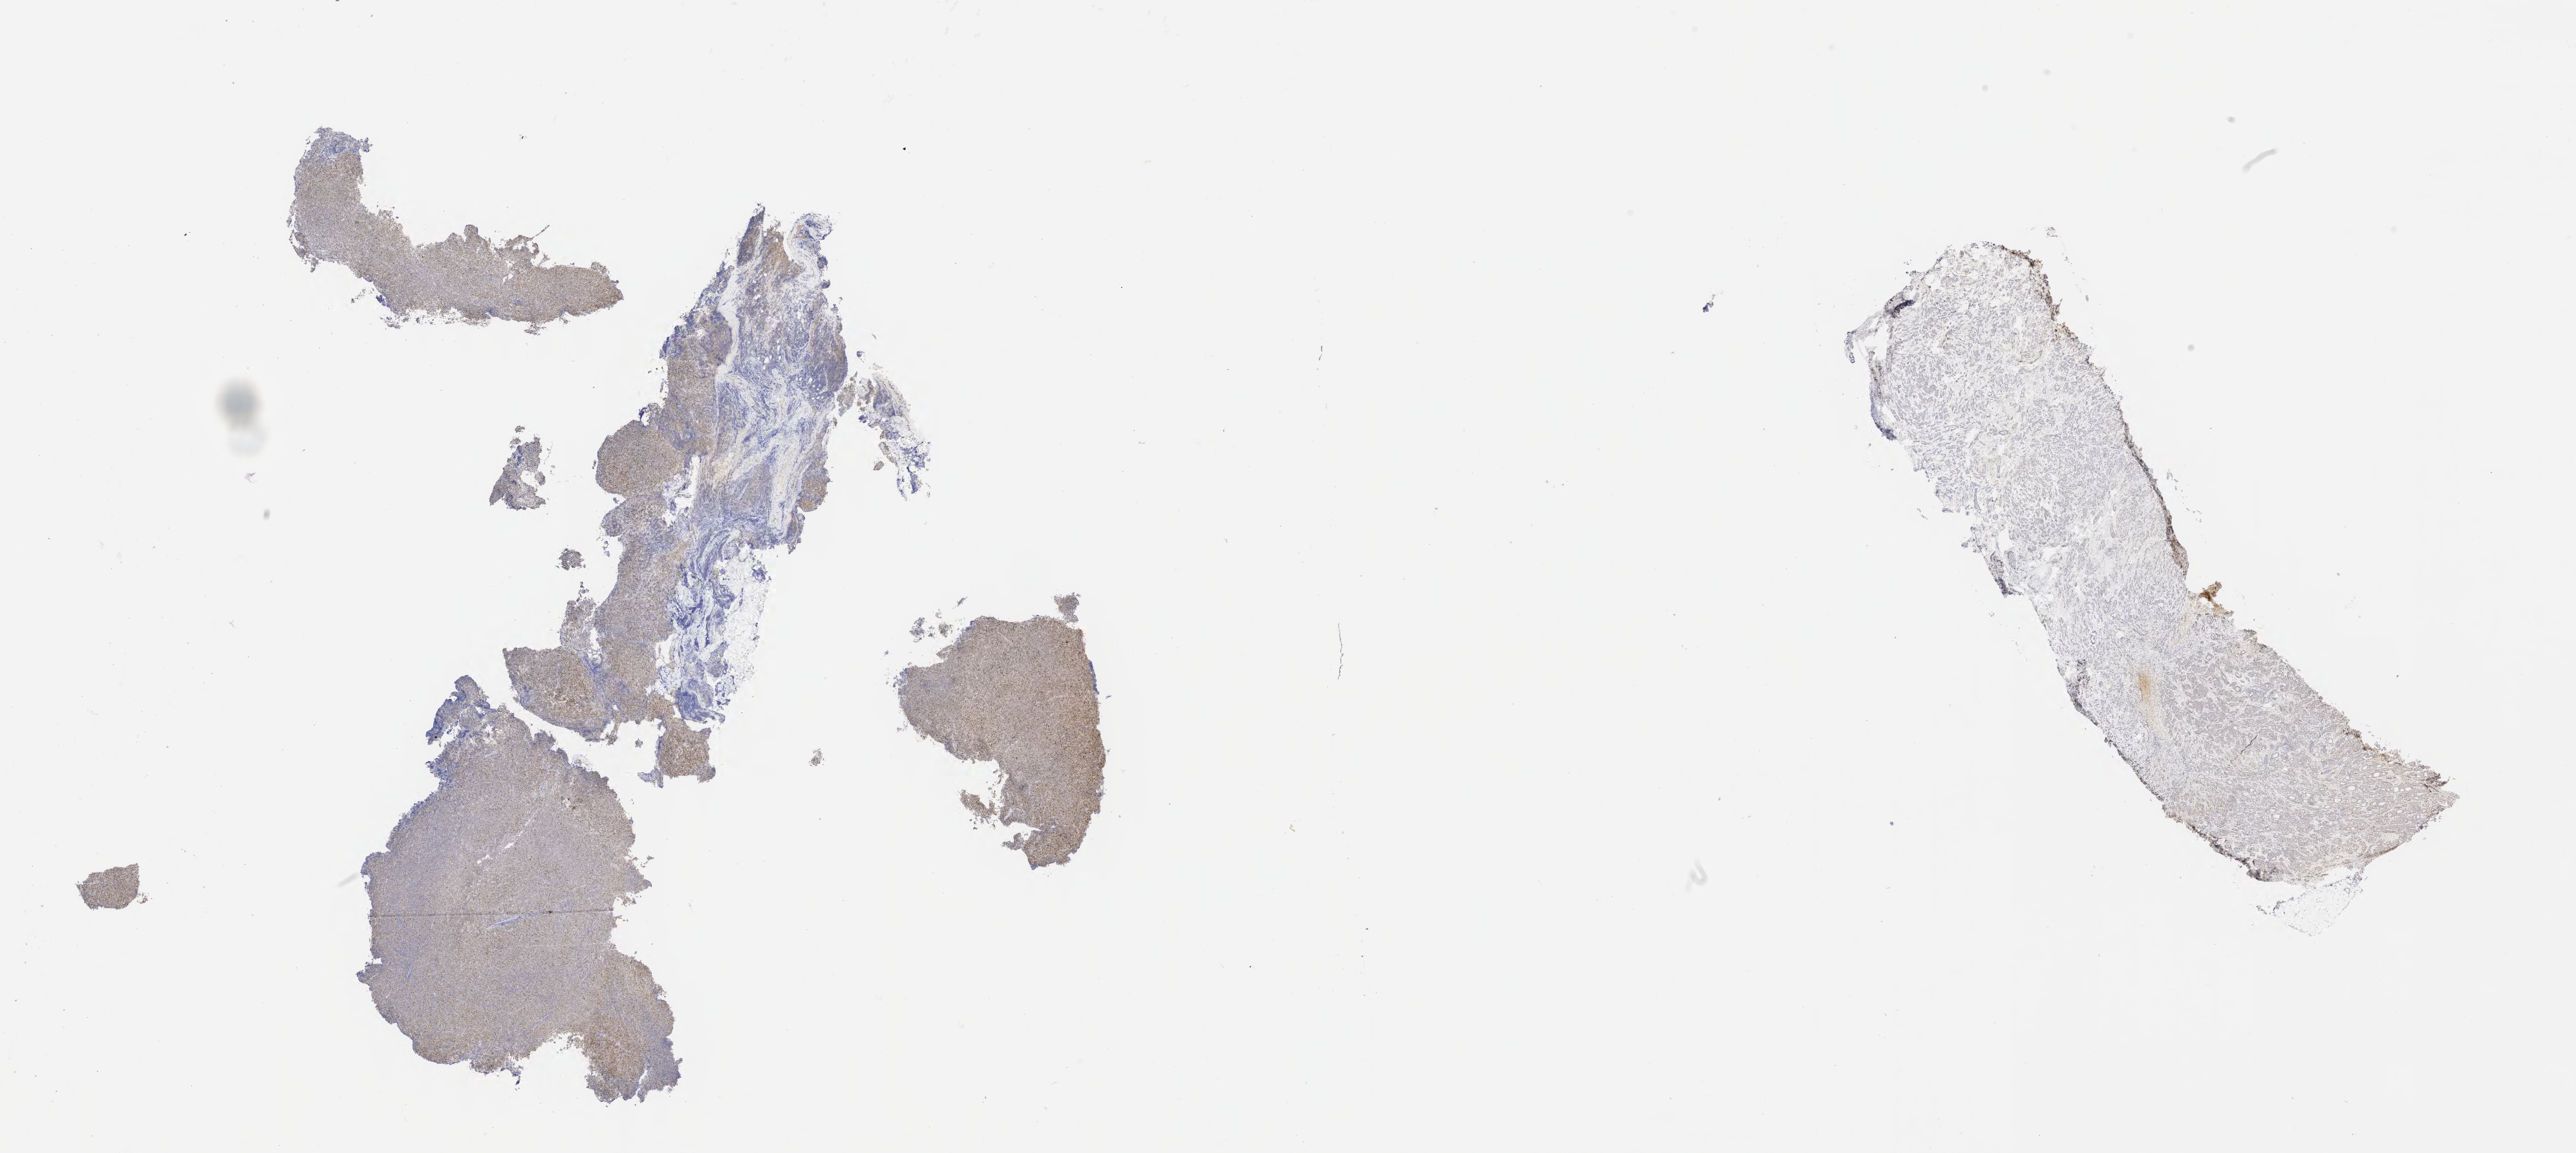
Whole-slide image, immunohistochemical stain for p53, low-resolution overview of the scanned area, about 32.2 x 14.4 mm; specimen: tumor tissue; site: liver. Patient female; 36 years old.
Diagnosis: Diffuse large B-cell lymphoma, NOS.